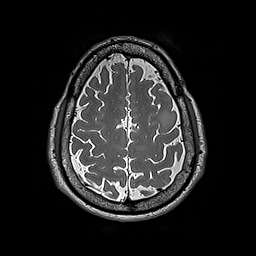
Brain MRI from a brain-tumour surgery series, one axial slice. Position 62 of 192 along the scan axis. 1 mm slice thickness. 256 × 256 image matrix, field of view 250 × 250 mm. From the clinical record (not read from this slice): histopathology: Astrocytoma; WHO grade: 2; IDH mutation: yes; tumour location: Left Frontal.
Structures marked on this image (expert manual segmentation):
- tumour: bounding box (x1, y1, x2, y2) in pixels: (158, 109, 174, 127)